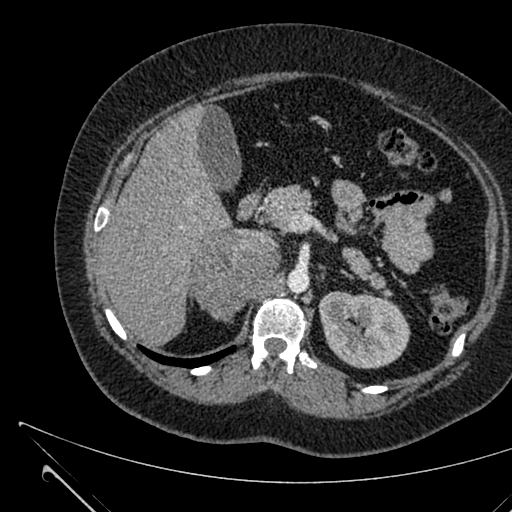
Contrast-enhanced abdominal CT, one axial slice; position 412 of 731 along the scan axis; 120 kVp; intravenous contrast given; soft-tissue window (W 400 / L 40 HU); 1 mm slice thickness; 512 × 512 image matrix, field of view 376 × 376 mm. Female patient, age 36 years. From the clinical record (not read from this slice): diagnosis: adrenocortical carcinoma; tumour side: right adrenal; tumour size at pathology: 10 cm; Ki-67 index: 20 %; stage (as recorded): 4.
Outlined on this slice (semi-automatically segmented with operator editing):
- mass: bounding box (x1, y1, x2, y2) in pixels: (195, 230, 276, 321)